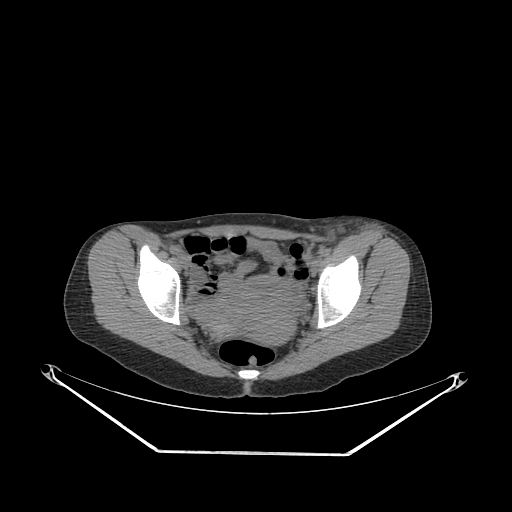
CT of an extremity soft-tissue mass (from a PET/CT study), one axial slice. Position 78 of 267 along the scan axis. Soft-tissue window (W 400 / L 40 HU). 3.75 mm slice thickness. 512 × 512 image matrix, field of view 500 × 500 mm. Female patient. Case-level facts recorded for this patient, not image findings: histological type: leiomyosarcoma; grade: high; site of the primary tumour: groin.
Structures marked on this image (expert contour drawn on MRI and transferred to this co-registered scan by the dataset authors):
- gross tumour volume including surrounding oedema: box from (x=322, y=228) to (x=391, y=255) px
- gross tumour volume (mass): (x=324, y=242)–(x=346, y=254)